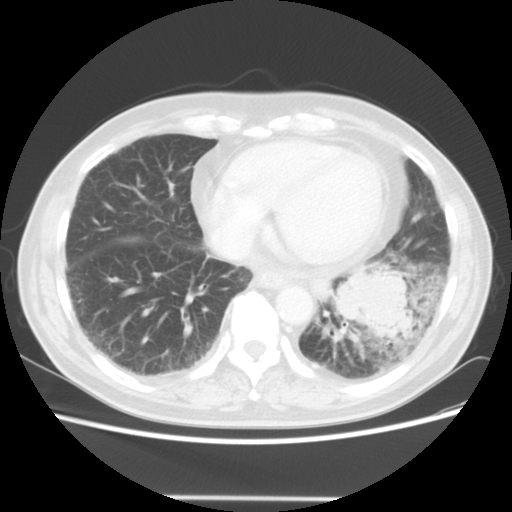
Chest CT, one axial slice; position 15 of 56 along the scan axis; 140 kVp; lung window (W 1500 / L -600 HU); 5 mm slice thickness; 512 × 512 image matrix, field of view 360 × 360 mm. Male patient, age 66 years. From the clinical record (not read from this slice): clinical TNM (as recorded): T4 N3 M0.
Annotated regions visible in this slice (rectangle marked by the reading radiologist):
- lung tumour (recorded histology: small cell carcinoma): box from (x=332, y=265) to (x=420, y=356) px